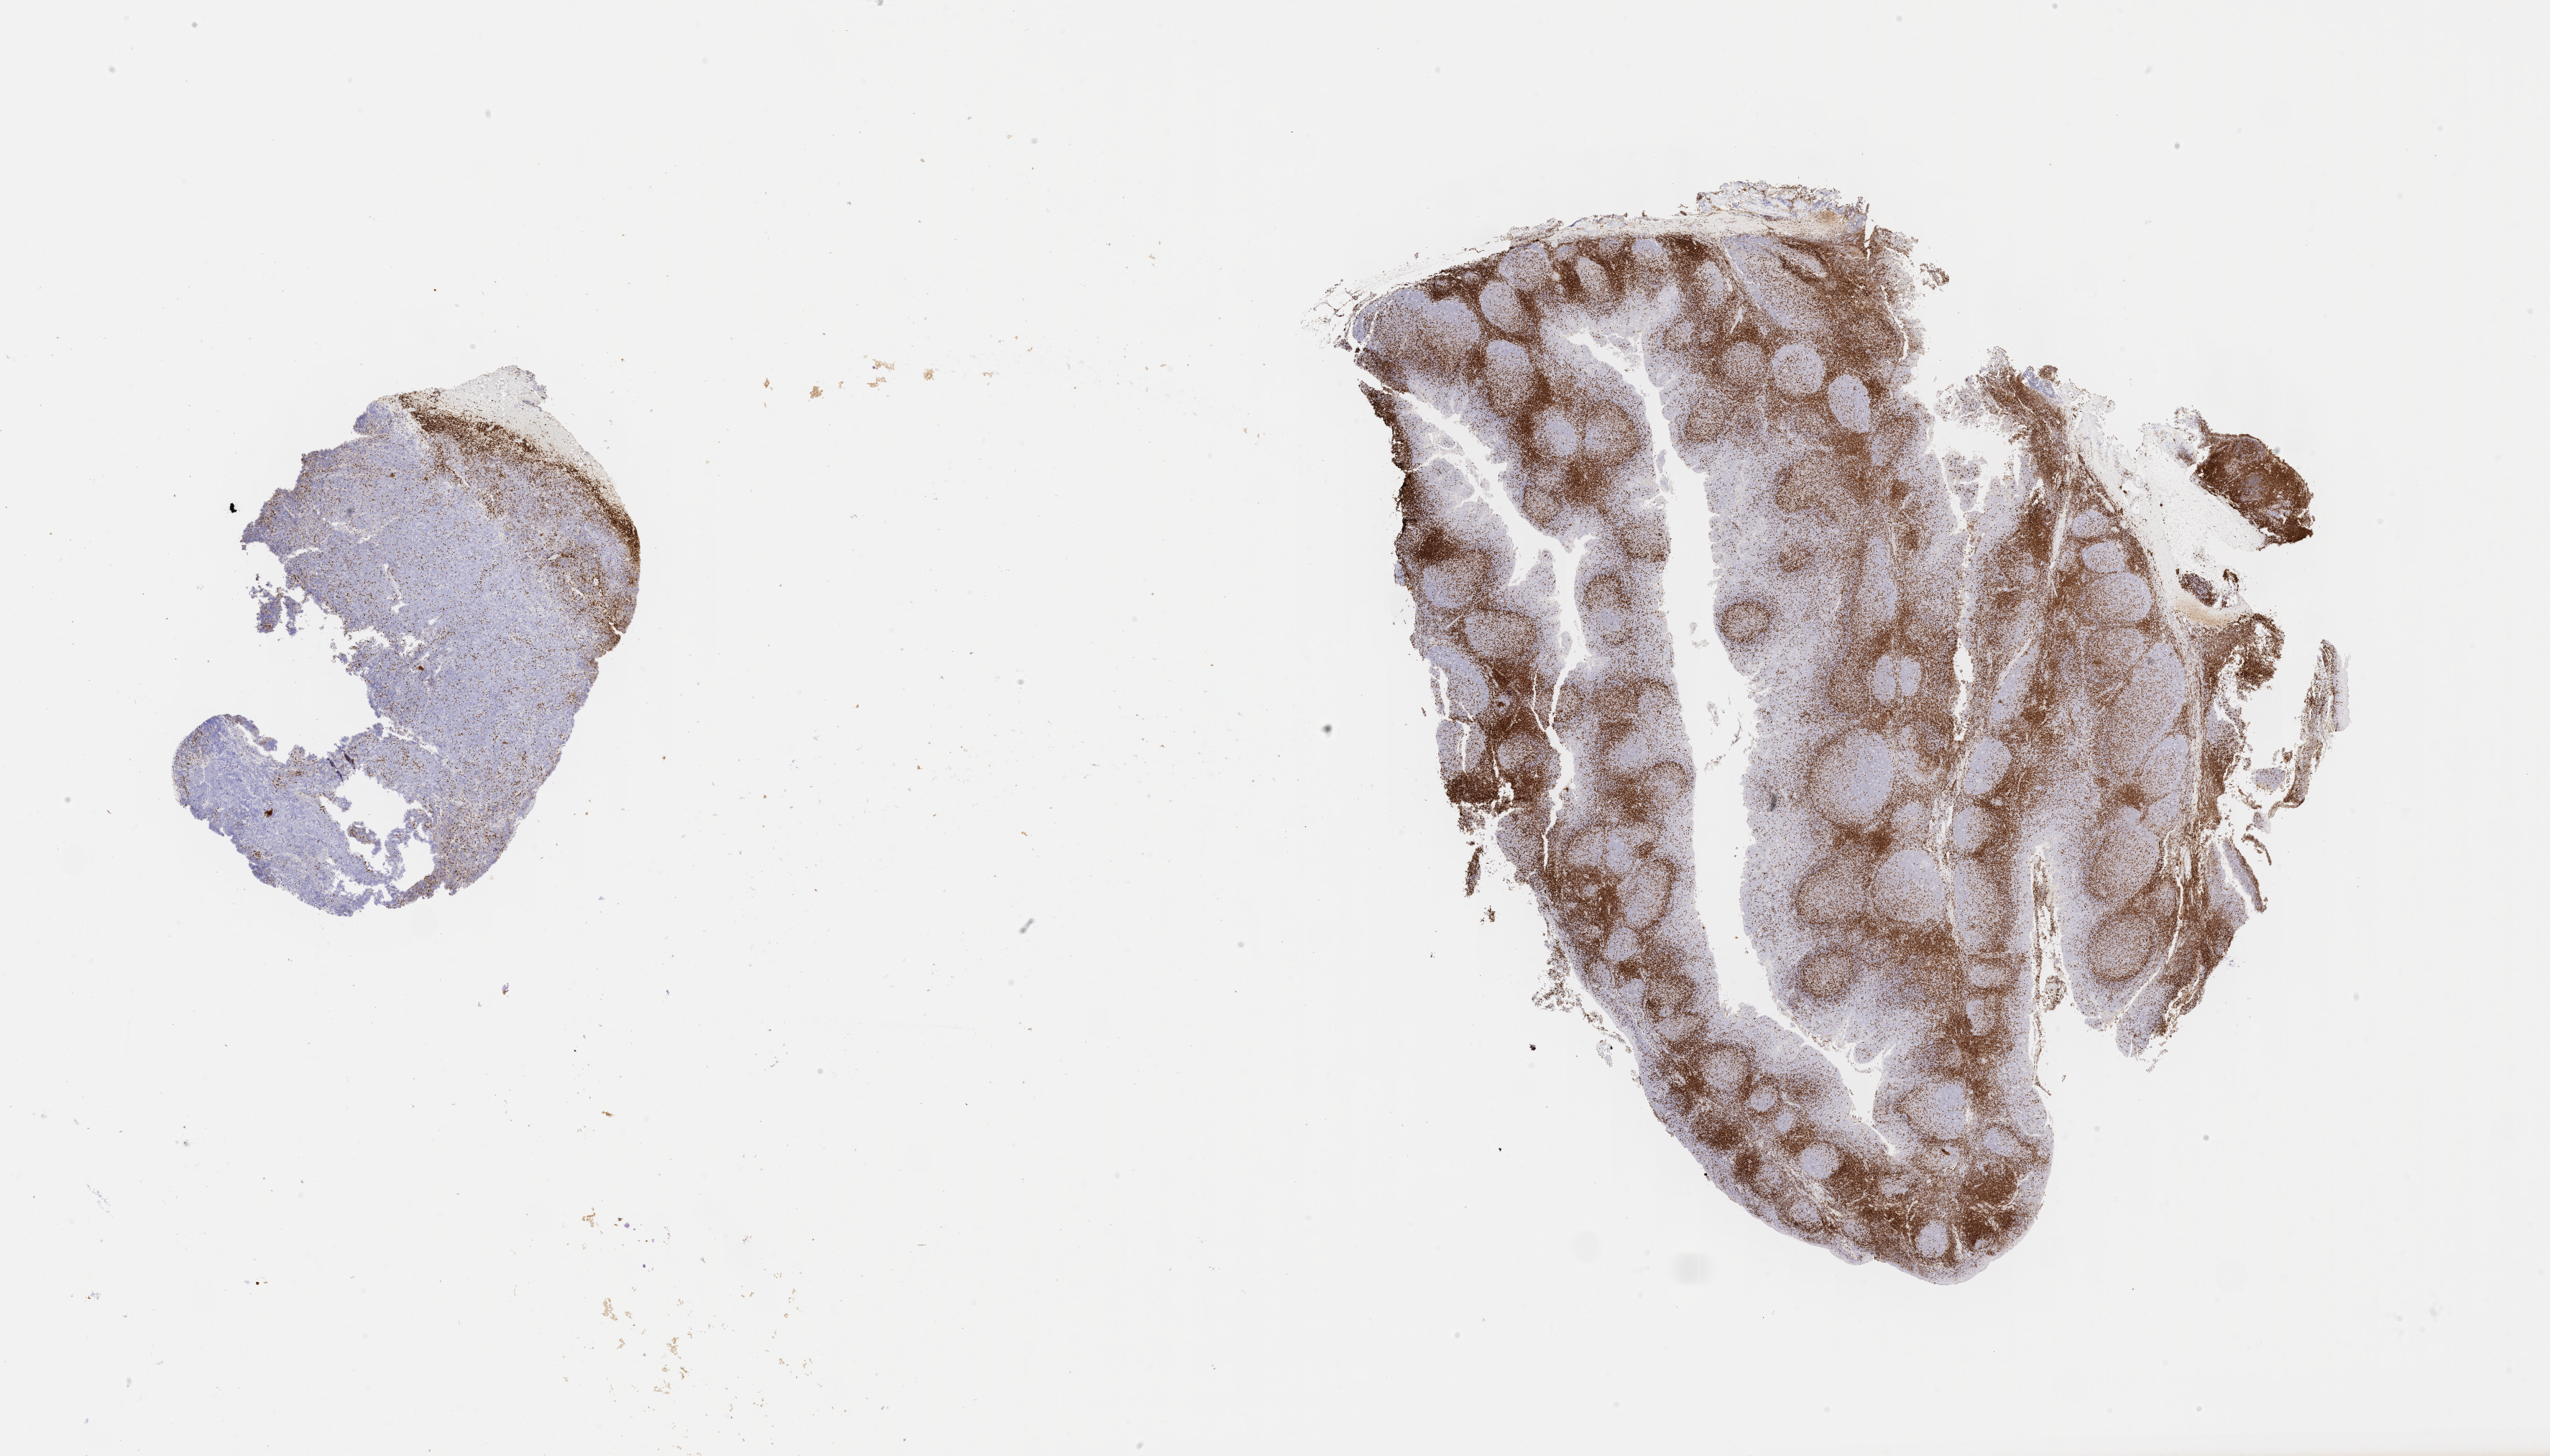
Immunohistochemistry (IHC) whole-slide image stained for CD3 — low-resolution overview of the scanned area, about 28.7 x 16.4 mm. Specimen: tumor tissue. Site: mandible. Female patient; age at initial diagnosis 7 years.
Diagnosis: Burkitt lymphoma, NOS.